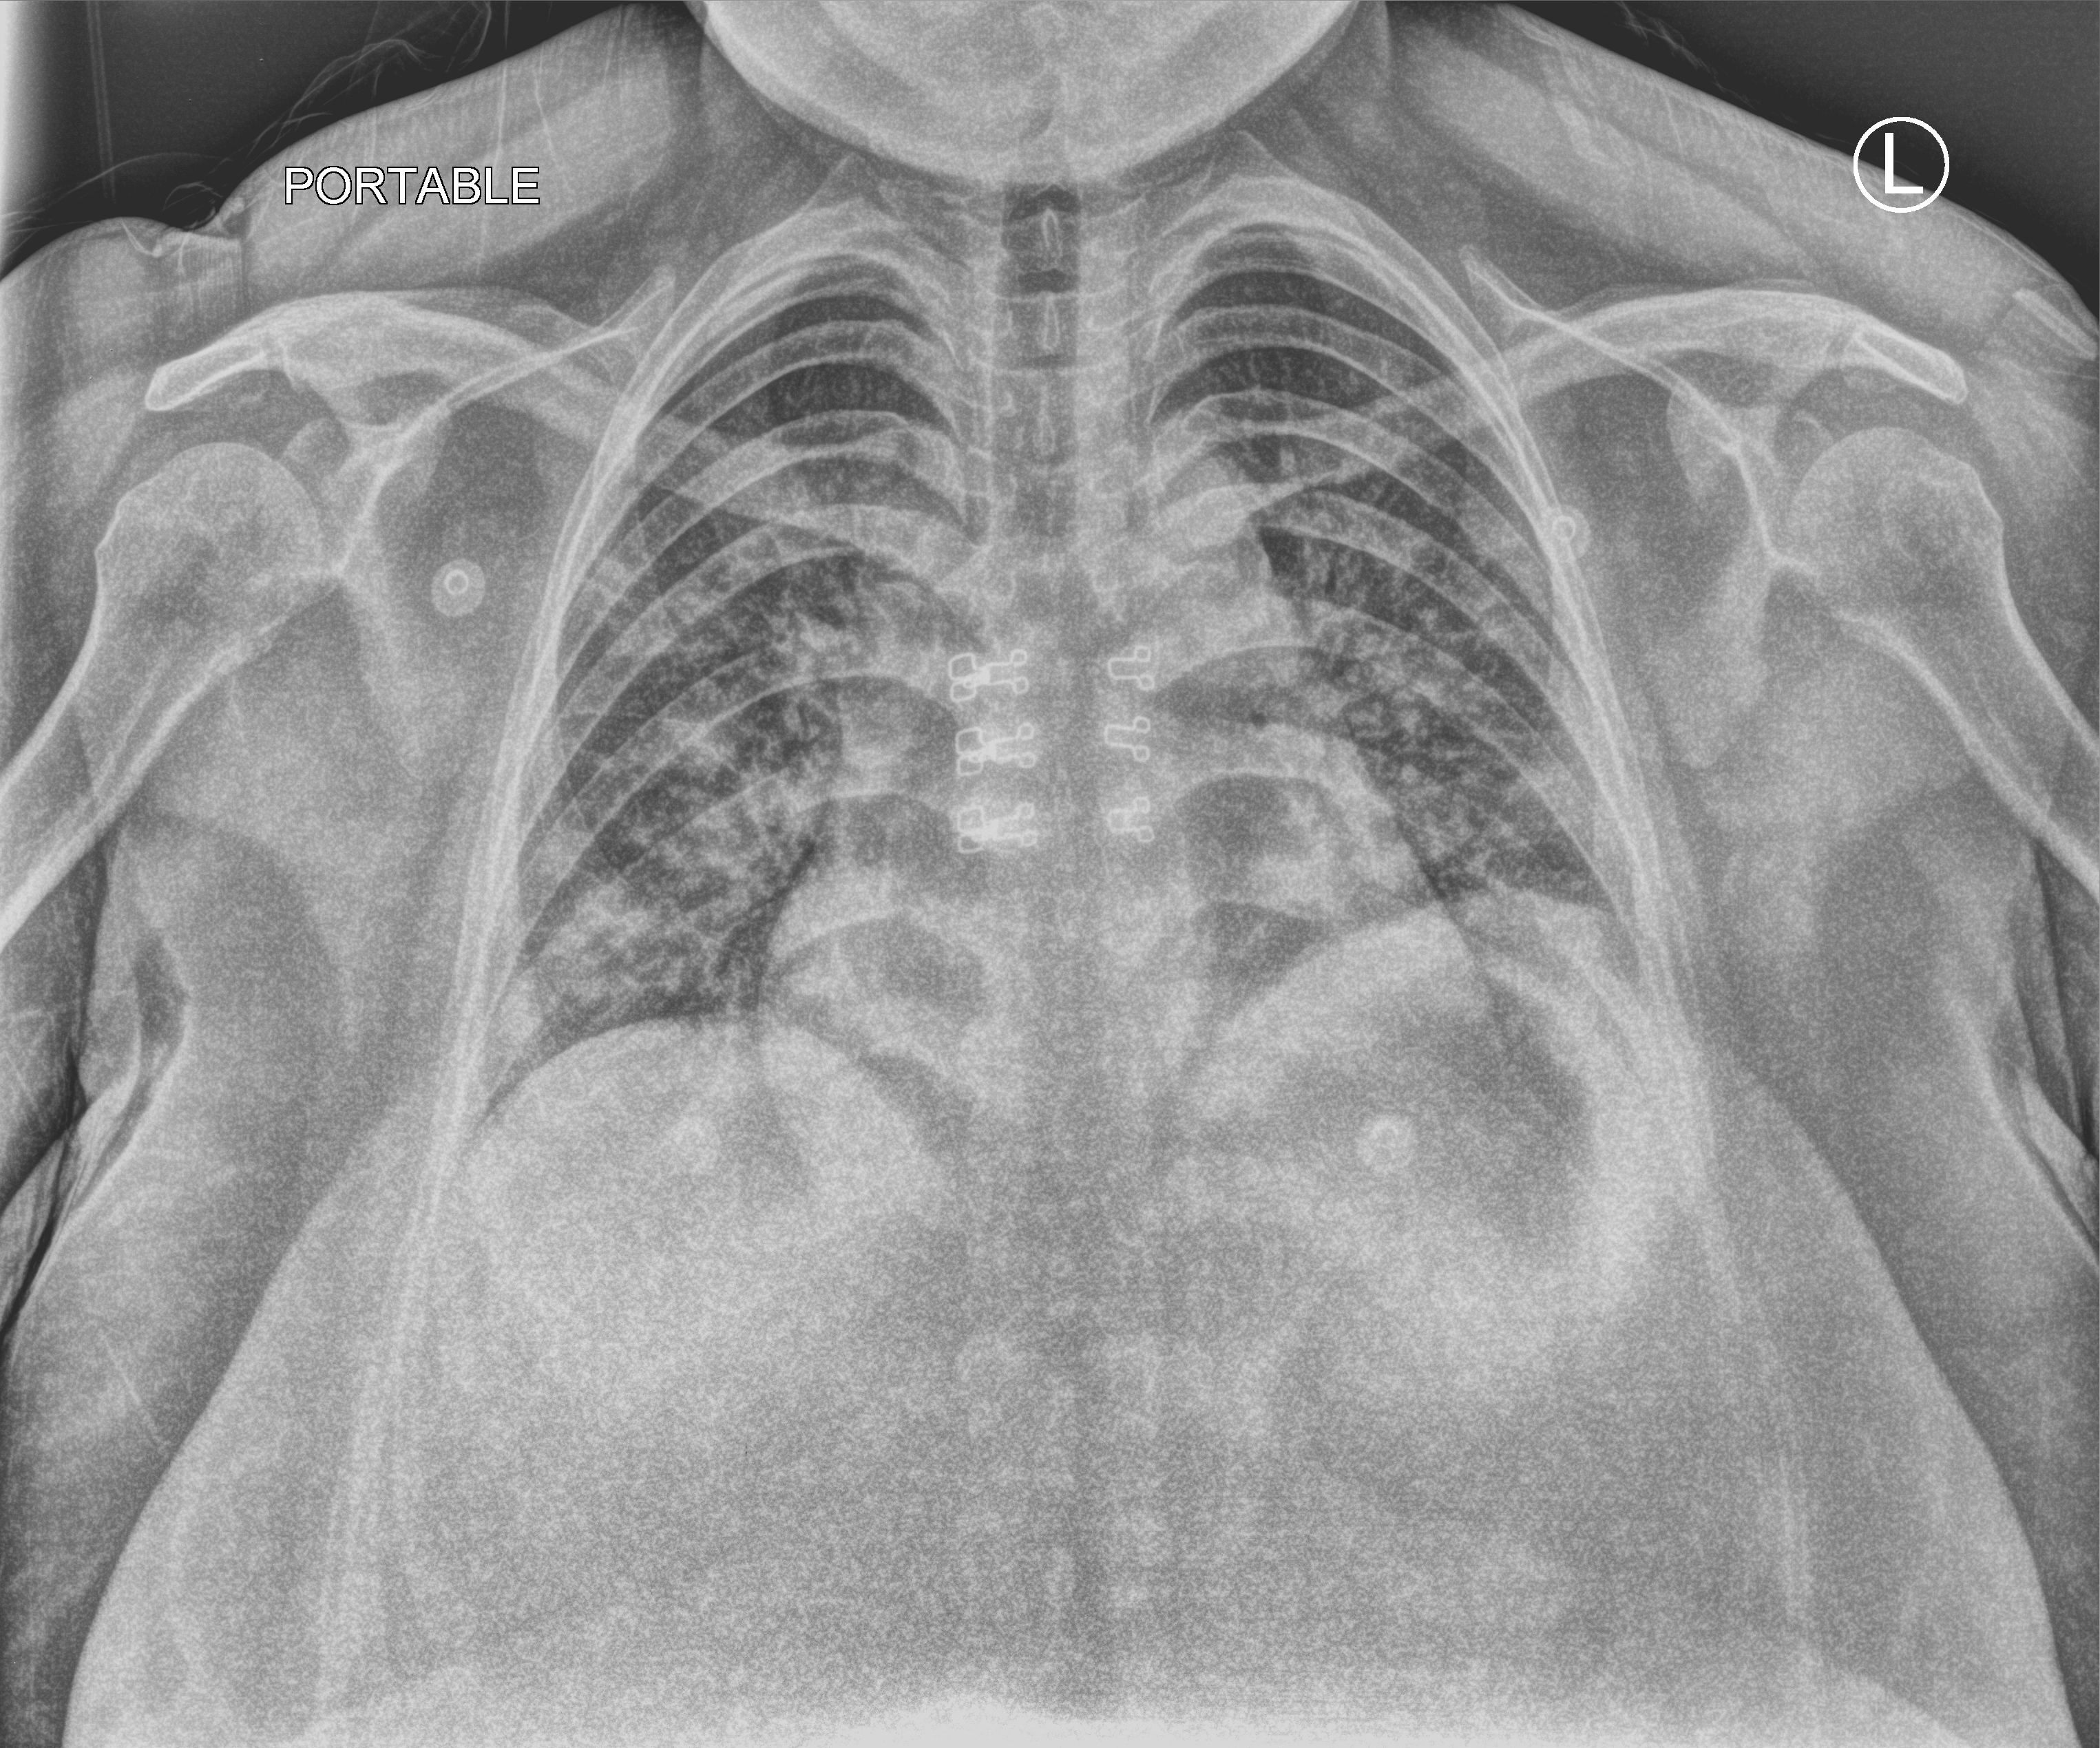
Bedside chest radiograph (computed radiography), anteroposterior (AP) projection. Patient hospitalised with COVID-19; female, aged 18–59 years.
From the hospital-stay record, not from the radiograph (when in the stay this image was taken is not recorded): mechanically ventilated during this hospital stay: no.